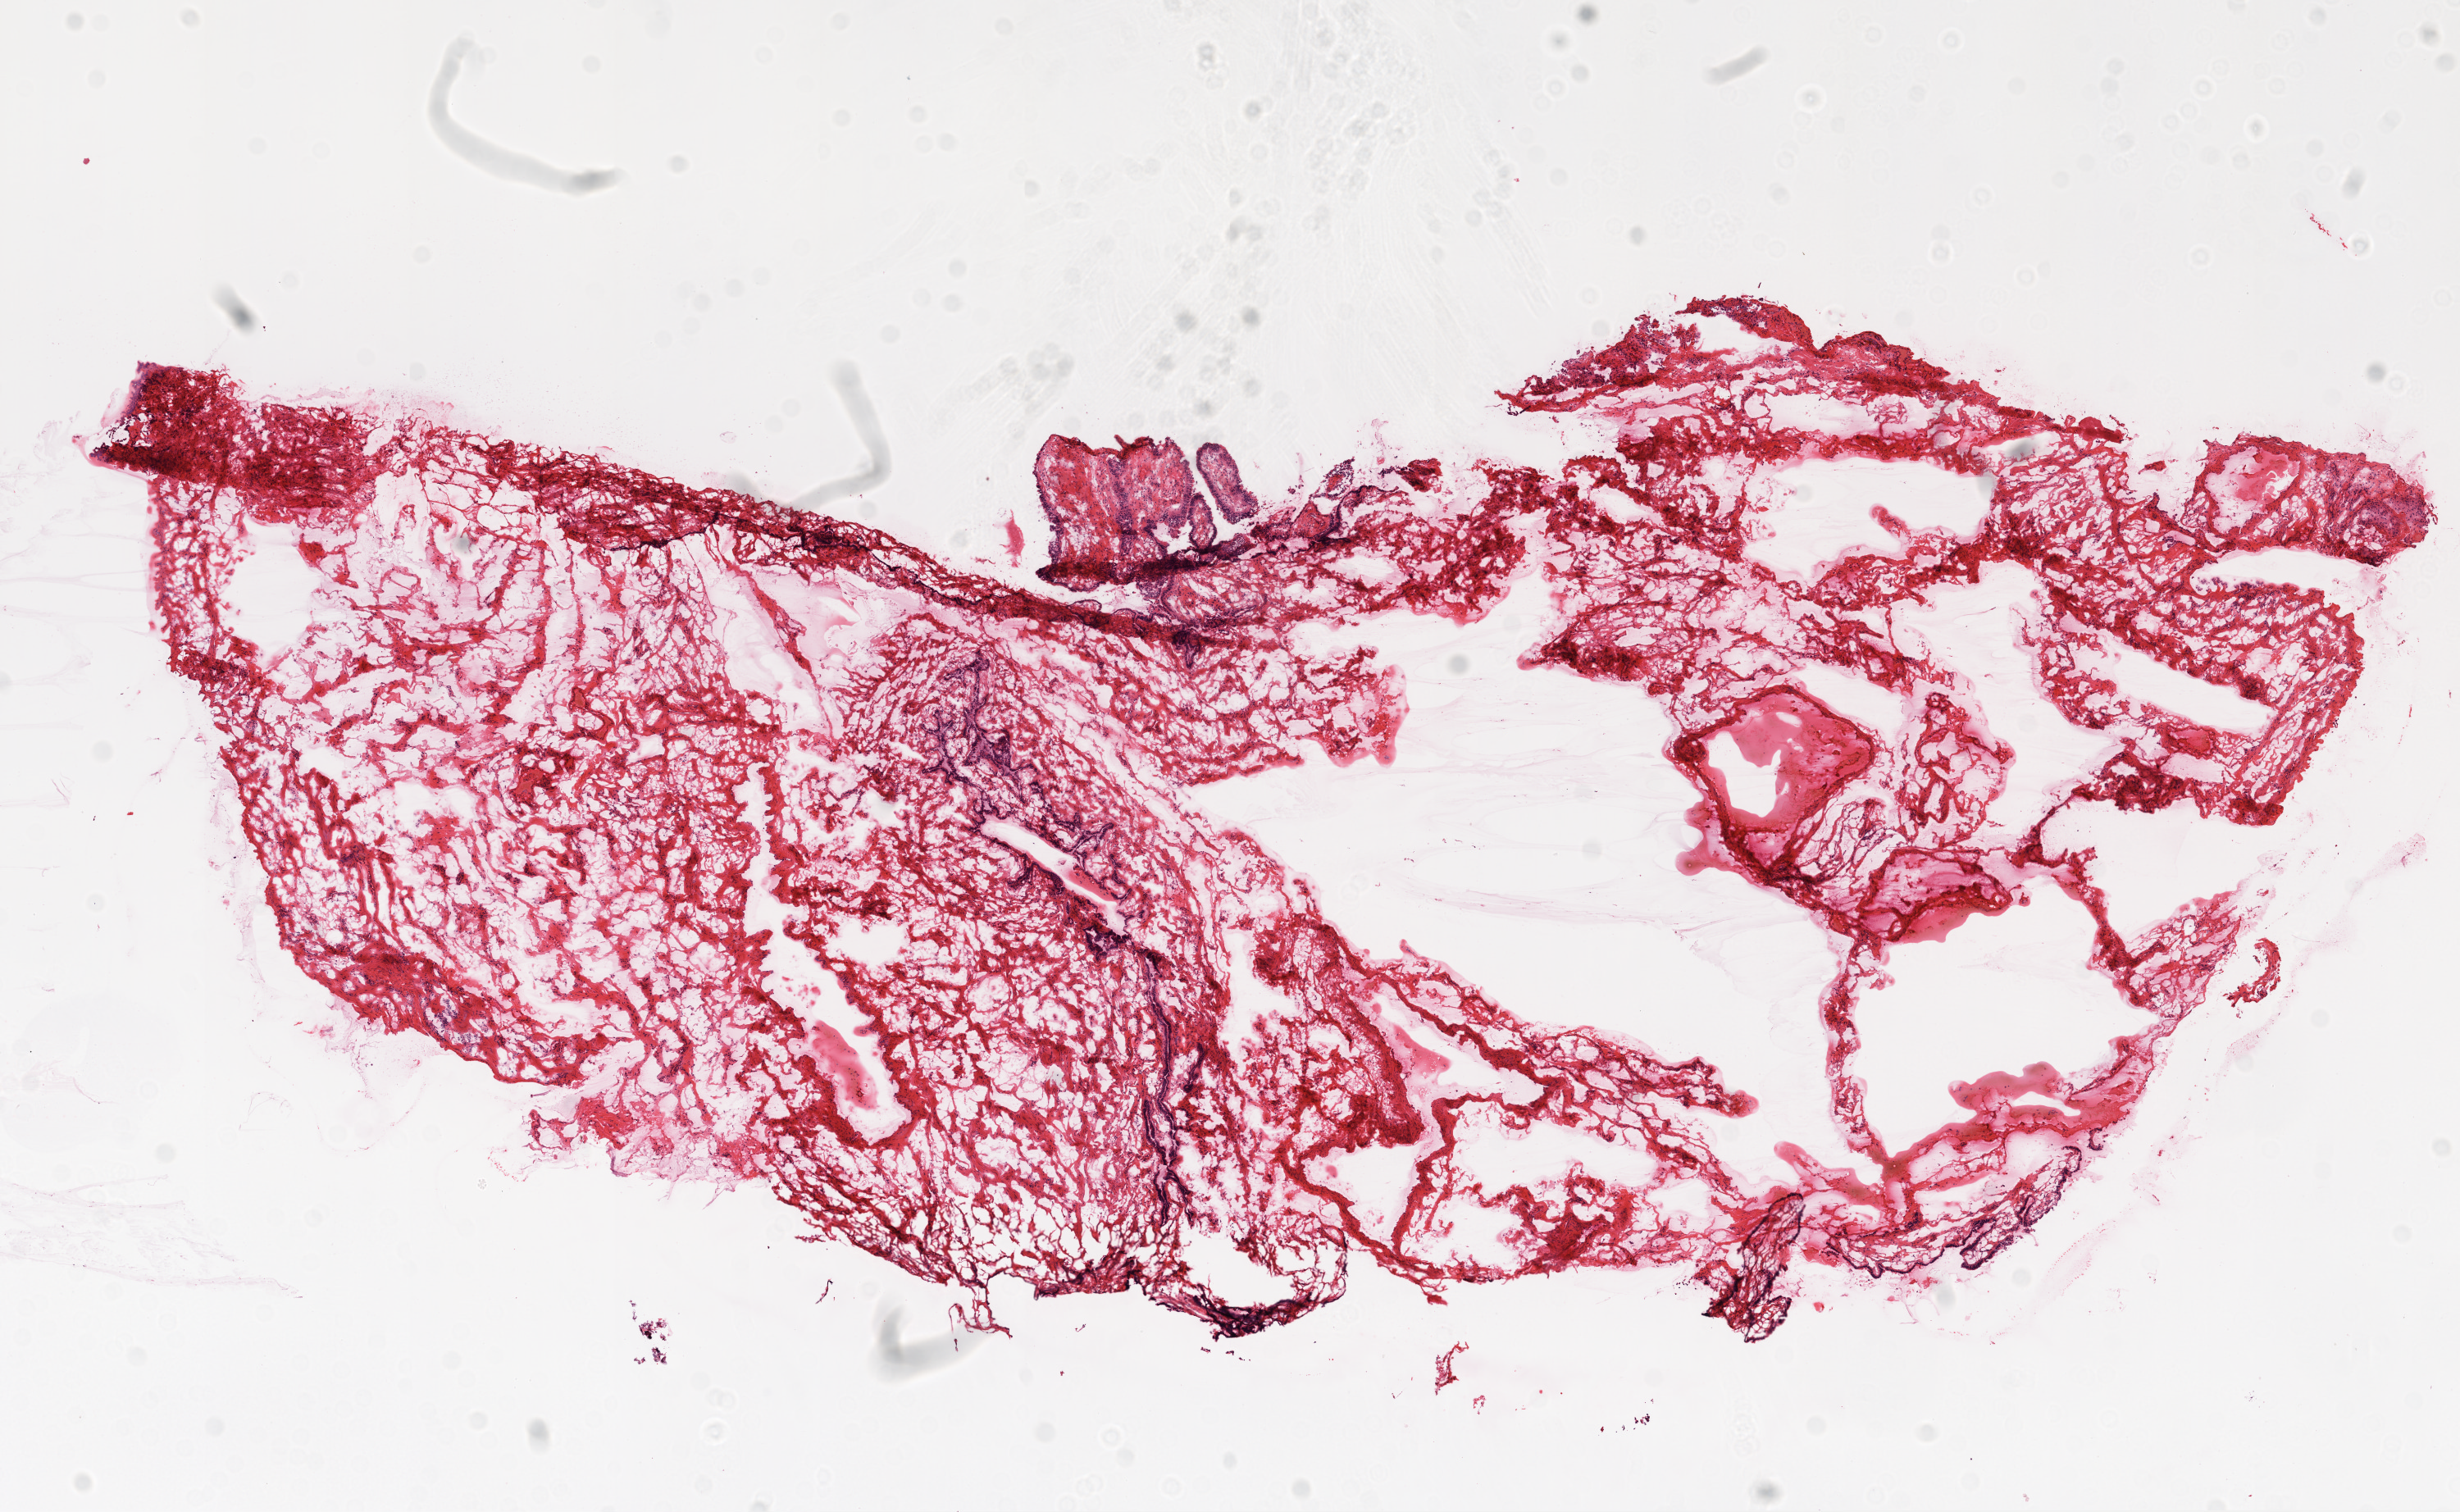
Digitized Hematoxylin and eosin (H&E) stained tissue section (whole slide), whole scanned area (about 12.0 x 7.4 mm, slide scanned at 20x) shown as a low-resolution overview, frozen section from the top of the tissue portion, sample: solid tissue normal (non-tumour tissue), ovary. Patient: female, age at initial diagnosis 62 years.
This section: solid tissue normal (non-tumour) sample from the same patient. Patient diagnosis: Serous cystadenocarcinoma, NOS.